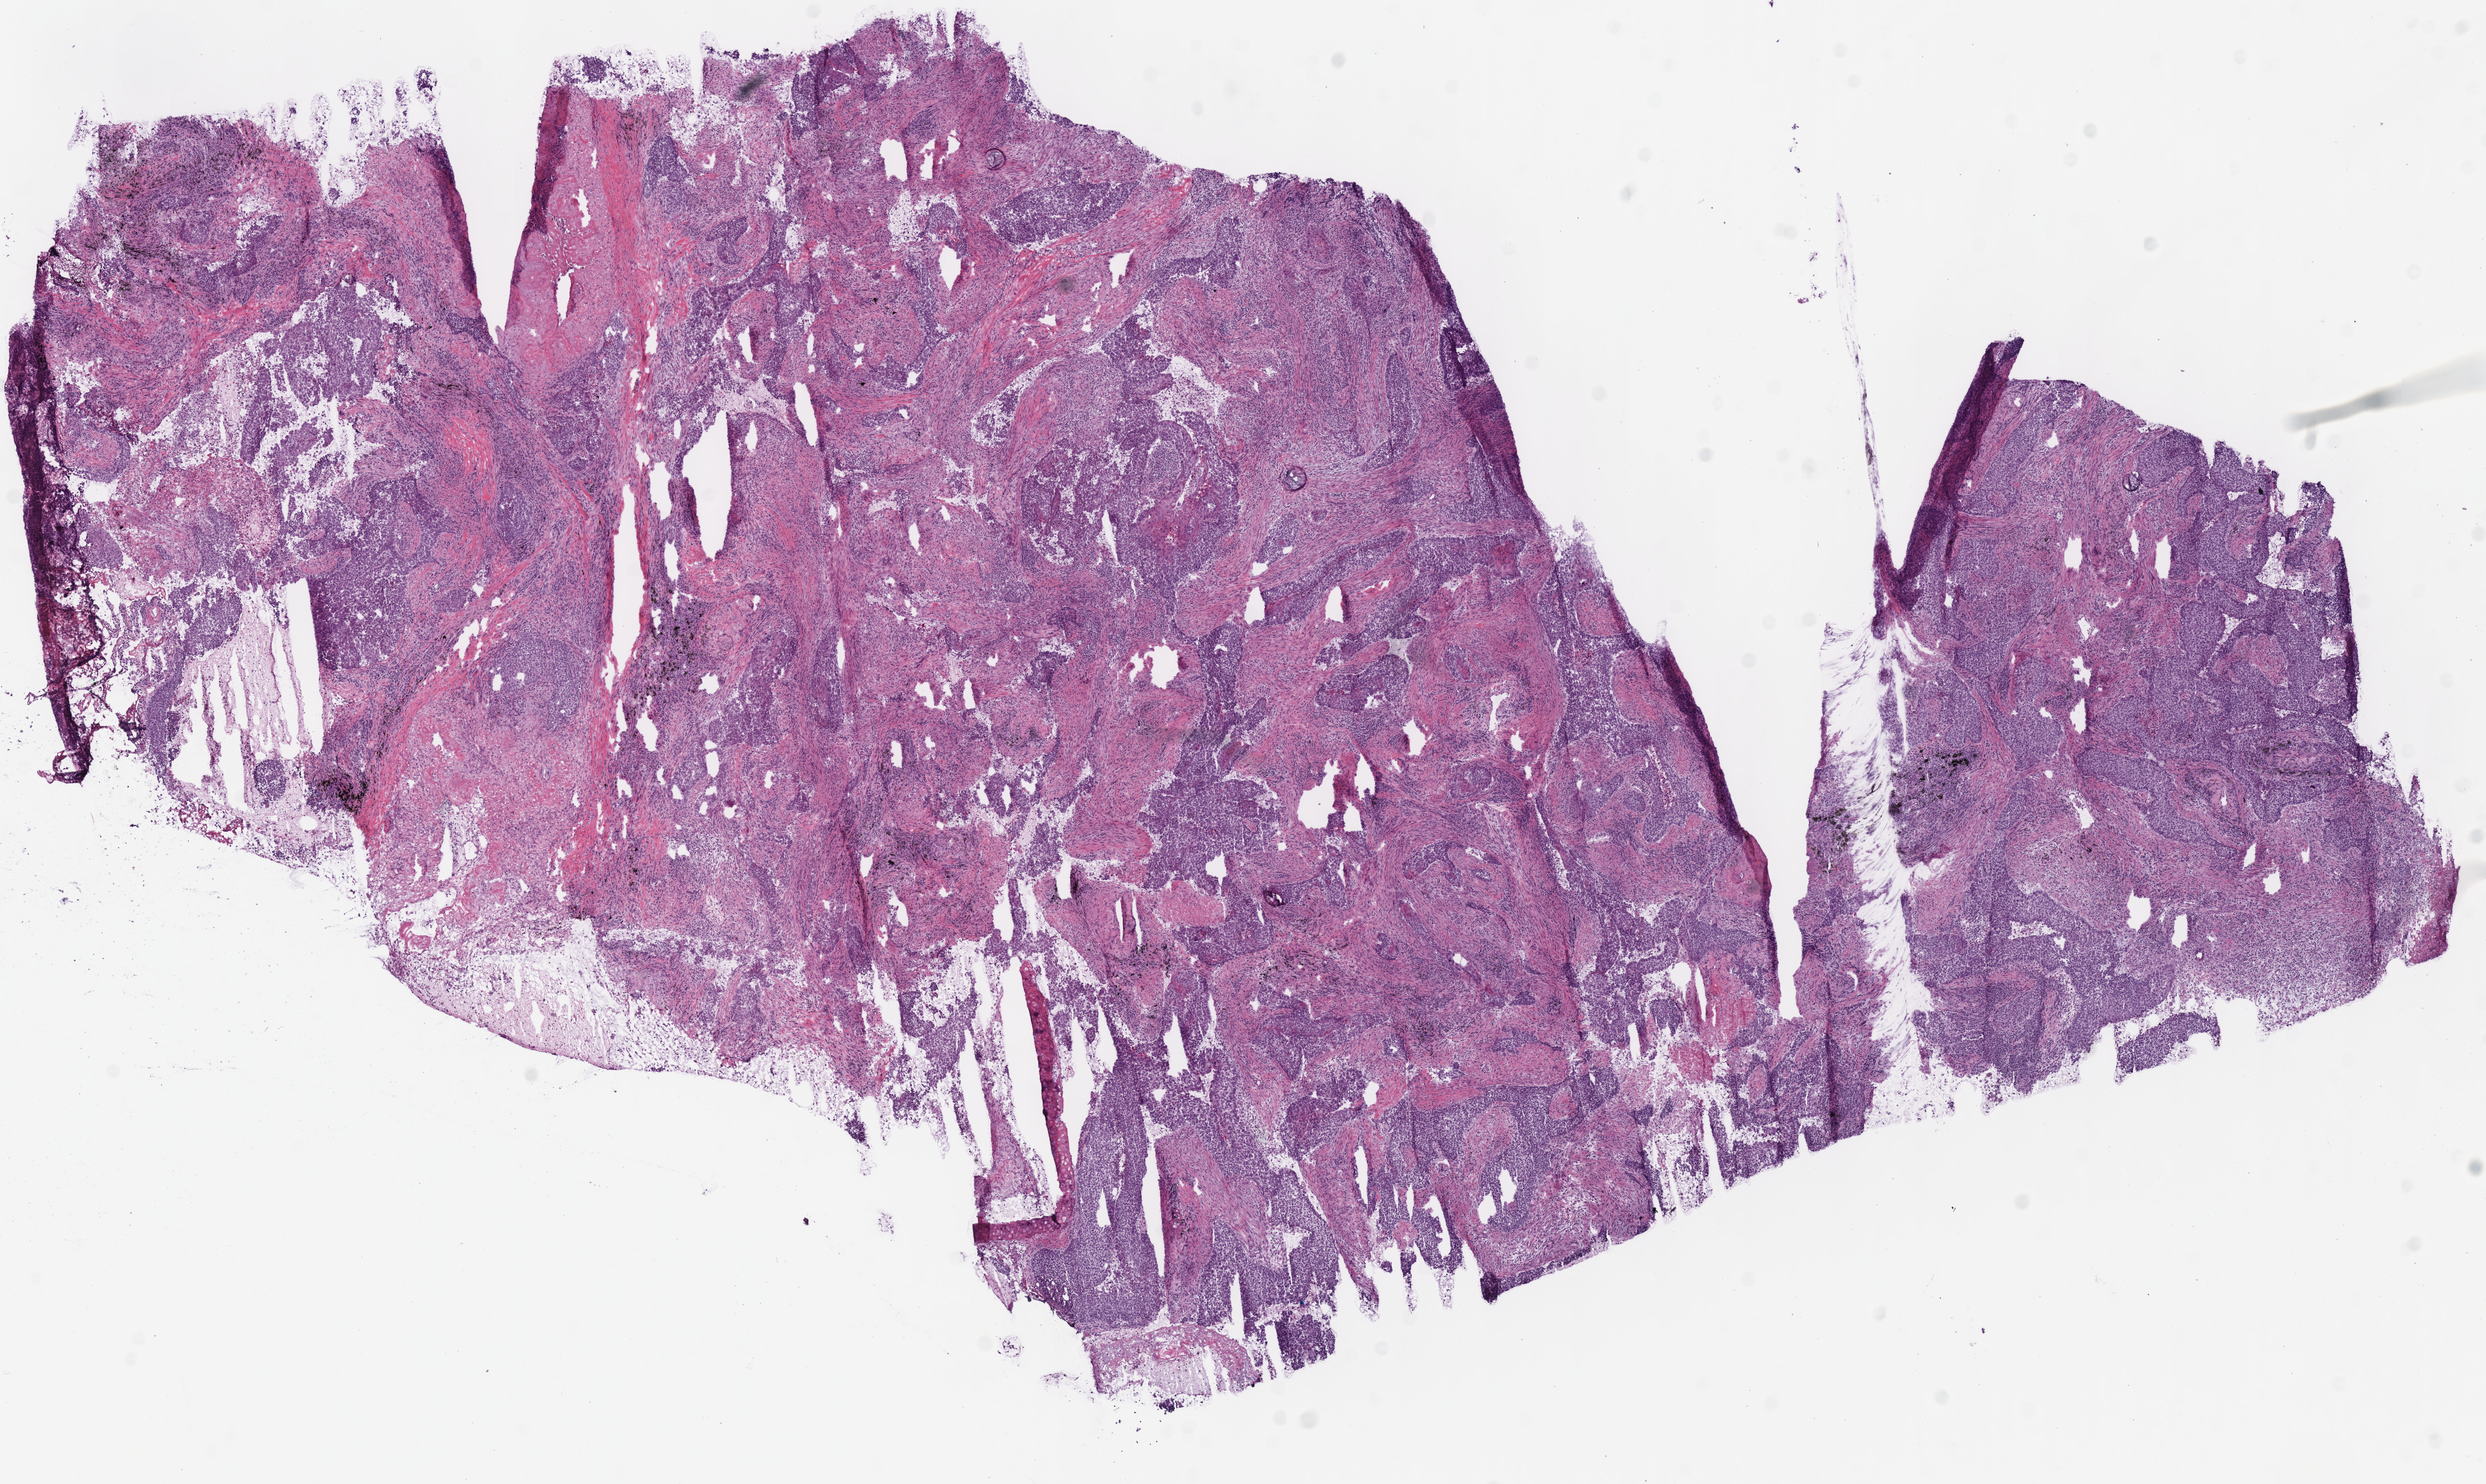
Digitized H&E tissue section (whole slide), a low-resolution overview of the entire scanned area, about 14.2 x 8.5 mm (acquisition: 40x scan). Frozen section from the bottom of the tissue portion. Lung, primary tumour sample. Female, age 72 years at initial diagnosis. Slide review estimates, as recorded: tumour cells 90%, tumour nuclei 65%, normal cells 0%, stromal cells 8%, necrosis 2%. Infiltration values recorded for this section: lymphocyte infiltration 20%, monocyte infiltration 0%, neutrophil infiltration 0%.
• AJCC pathologic stage: IIA
• laterality: left
• diagnosis: Squamous cell carcinoma, NOS (lower lobe, lung)